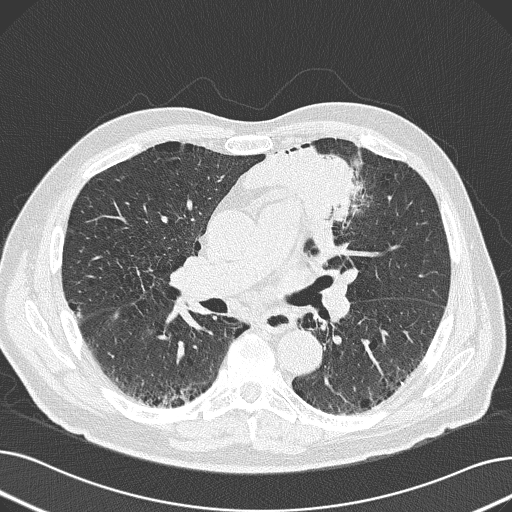
Chest CT (low-dose screening protocol), one axial image. Baseline annual screen. Lung window (W 1500 / L -600 HU). 2 mm slice thickness. Lung (sharp) reconstruction kernel (B50f). 120 kVp. Slice 82 of 165 in the series. 512 × 512 image matrix, field of view 370 × 370 mm. Male participant, aged 69 years at enrolment.
- Expert-annotated lung lesion, box from (x=239, y=128) to (x=386, y=248) px.
- Reader record for this screening exam (exam-level; its link to the box is not recorded): non-calcified nodule or mass ≥4 mm, left upper lobe, 6 × 10 mm, spiculated (stellate) margins, soft tissue attenuation.
- Official screen result: positive, change unspecified: nodule(s) >= 4 mm or enlarging nodule(s), mass(es), or other non-specific abnormalities suspicious for lung cancer.